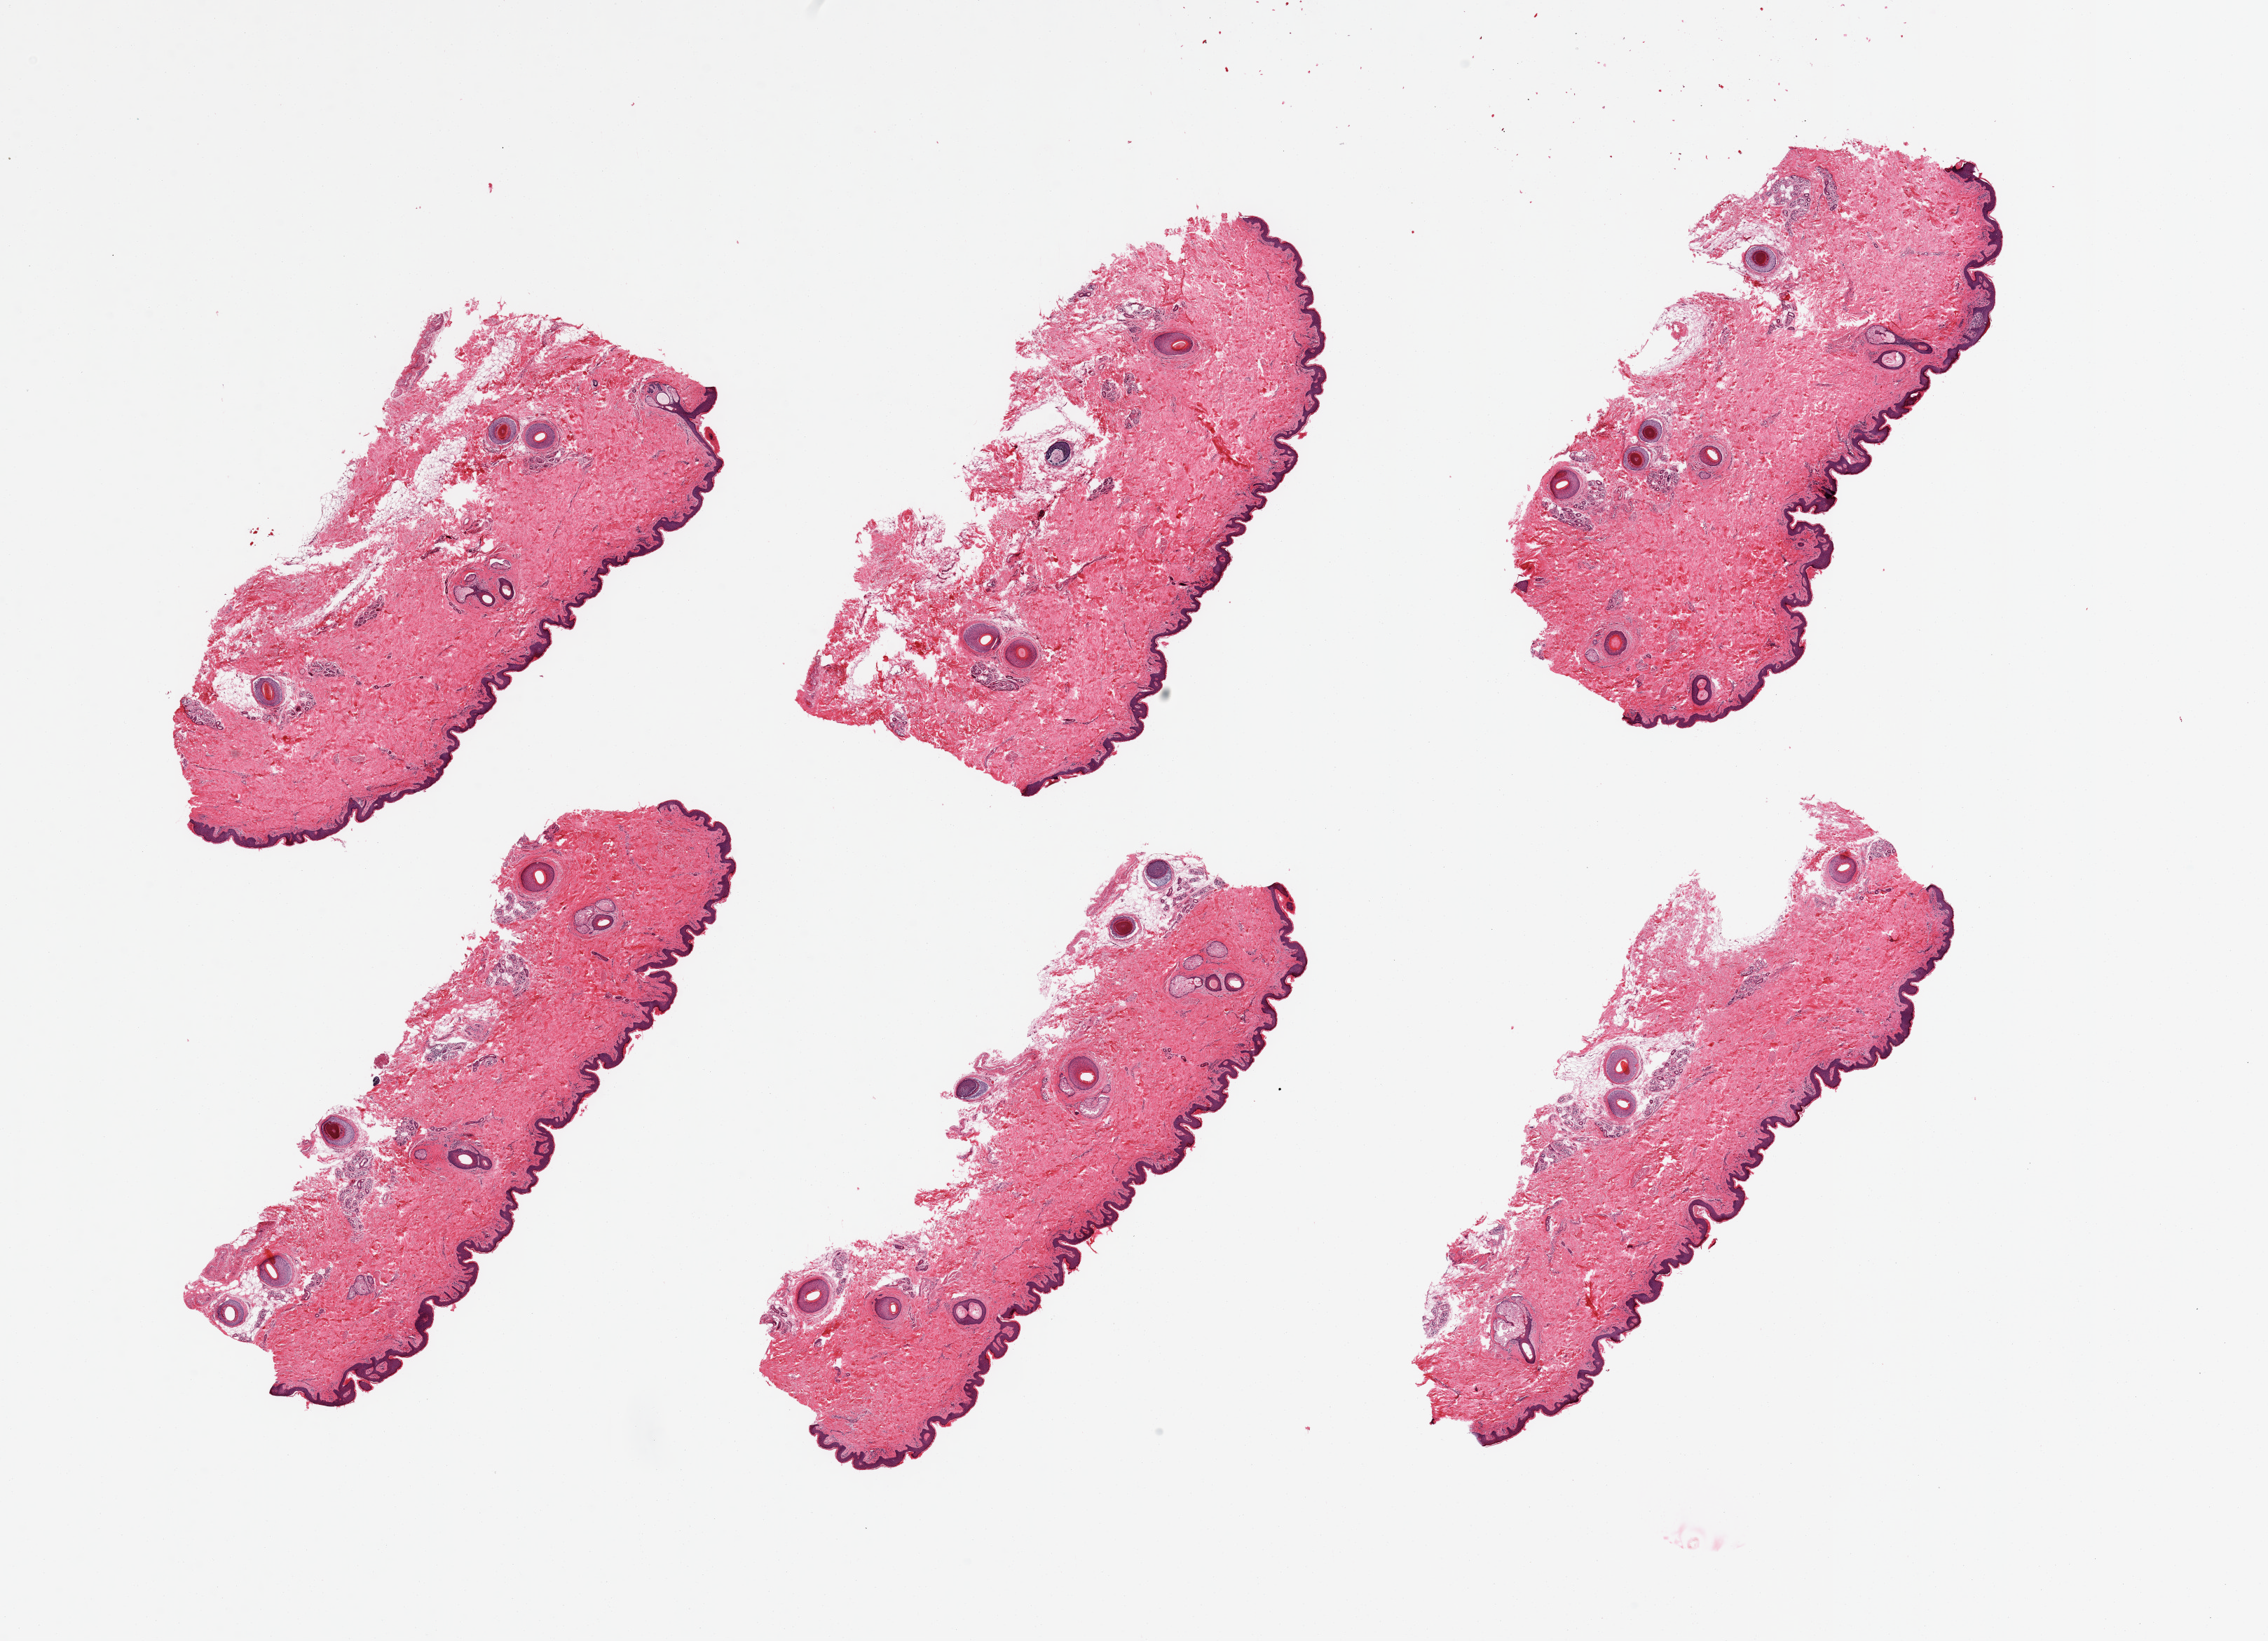
Haematoxylin and eosin whole-slide image, whole scanned area (about 25.6 x 18.5 mm) shown as a low-resolution overview. PAXgene-fixed paraffin-embedded (PFPE) section. Target tissue: skin of suprapubic region. Tissue donor sample.
Pathologist's review note for this sample: 6 pieces; well-trimmed hair-bearing skin; 10% dermal fat.